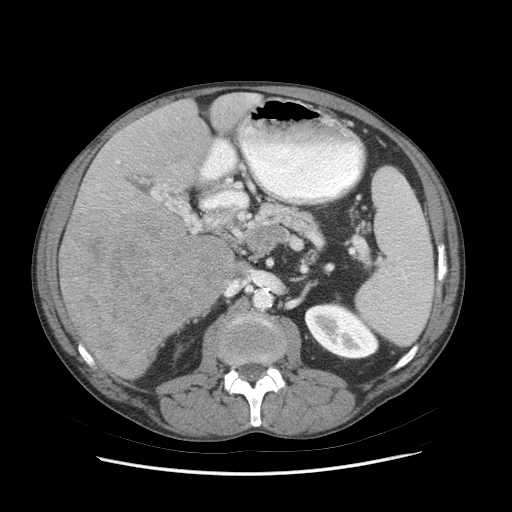
Contrast-enhanced abdominal CT (liver protocol), one axial slice. Position 35 of 89 along the scan axis. Reconstruction kernel STANDARD. Soft-tissue window (W 400 / L 40 HU). 512 × 512 image matrix. From the clinical record (not read from this slice): diagnosis: hepatocellular carcinoma (patient treated with transarterial chemoembolisation; whether this scan precedes or follows treatment is not stated here); TNM stage (as recorded): Stage-IIIB; Child-Pugh class: A; tumour differentiation: moderately differentiated; tumour nodularity: multinodular.
Annotated regions visible in this slice (semi-automatic segmentation, software-assisted and operator-edited):
- liver parenchyma outside the tumour (the mass and vessels are separate outlines, so this box may not span the whole liver): bounding box [x1, y1, x2, y2] px = [58, 92, 262, 380]
- mass: [61, 207, 235, 379]
- liver vessels: [117, 94, 259, 199]